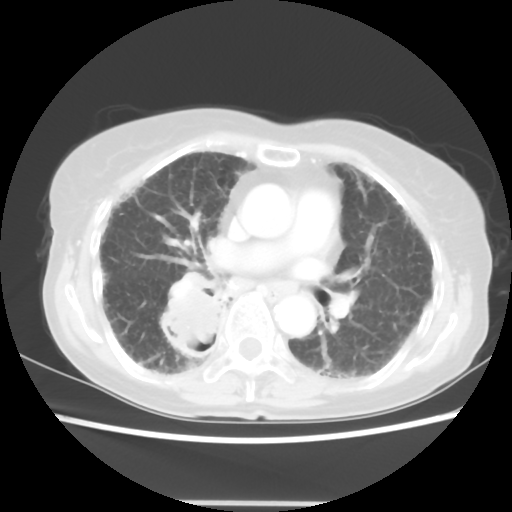
Chest CT, one axial slice; position 28 of 52 along the scan axis; reconstruction kernel STANDARD; 120 kVp; lung window (W 1500 / L -600 HU); 512 × 512 image matrix. Female patient, age 71 years. Case-level facts recorded for this patient, not image findings: clinical TNM (as recorded): T3 N0 M0.
Annotated regions visible in this slice (bounding box drawn by a radiologist):
- lung tumour (recorded histology: squamous cell carcinoma): bounding box [x1, y1, x2, y2] px = [163, 285, 228, 358]